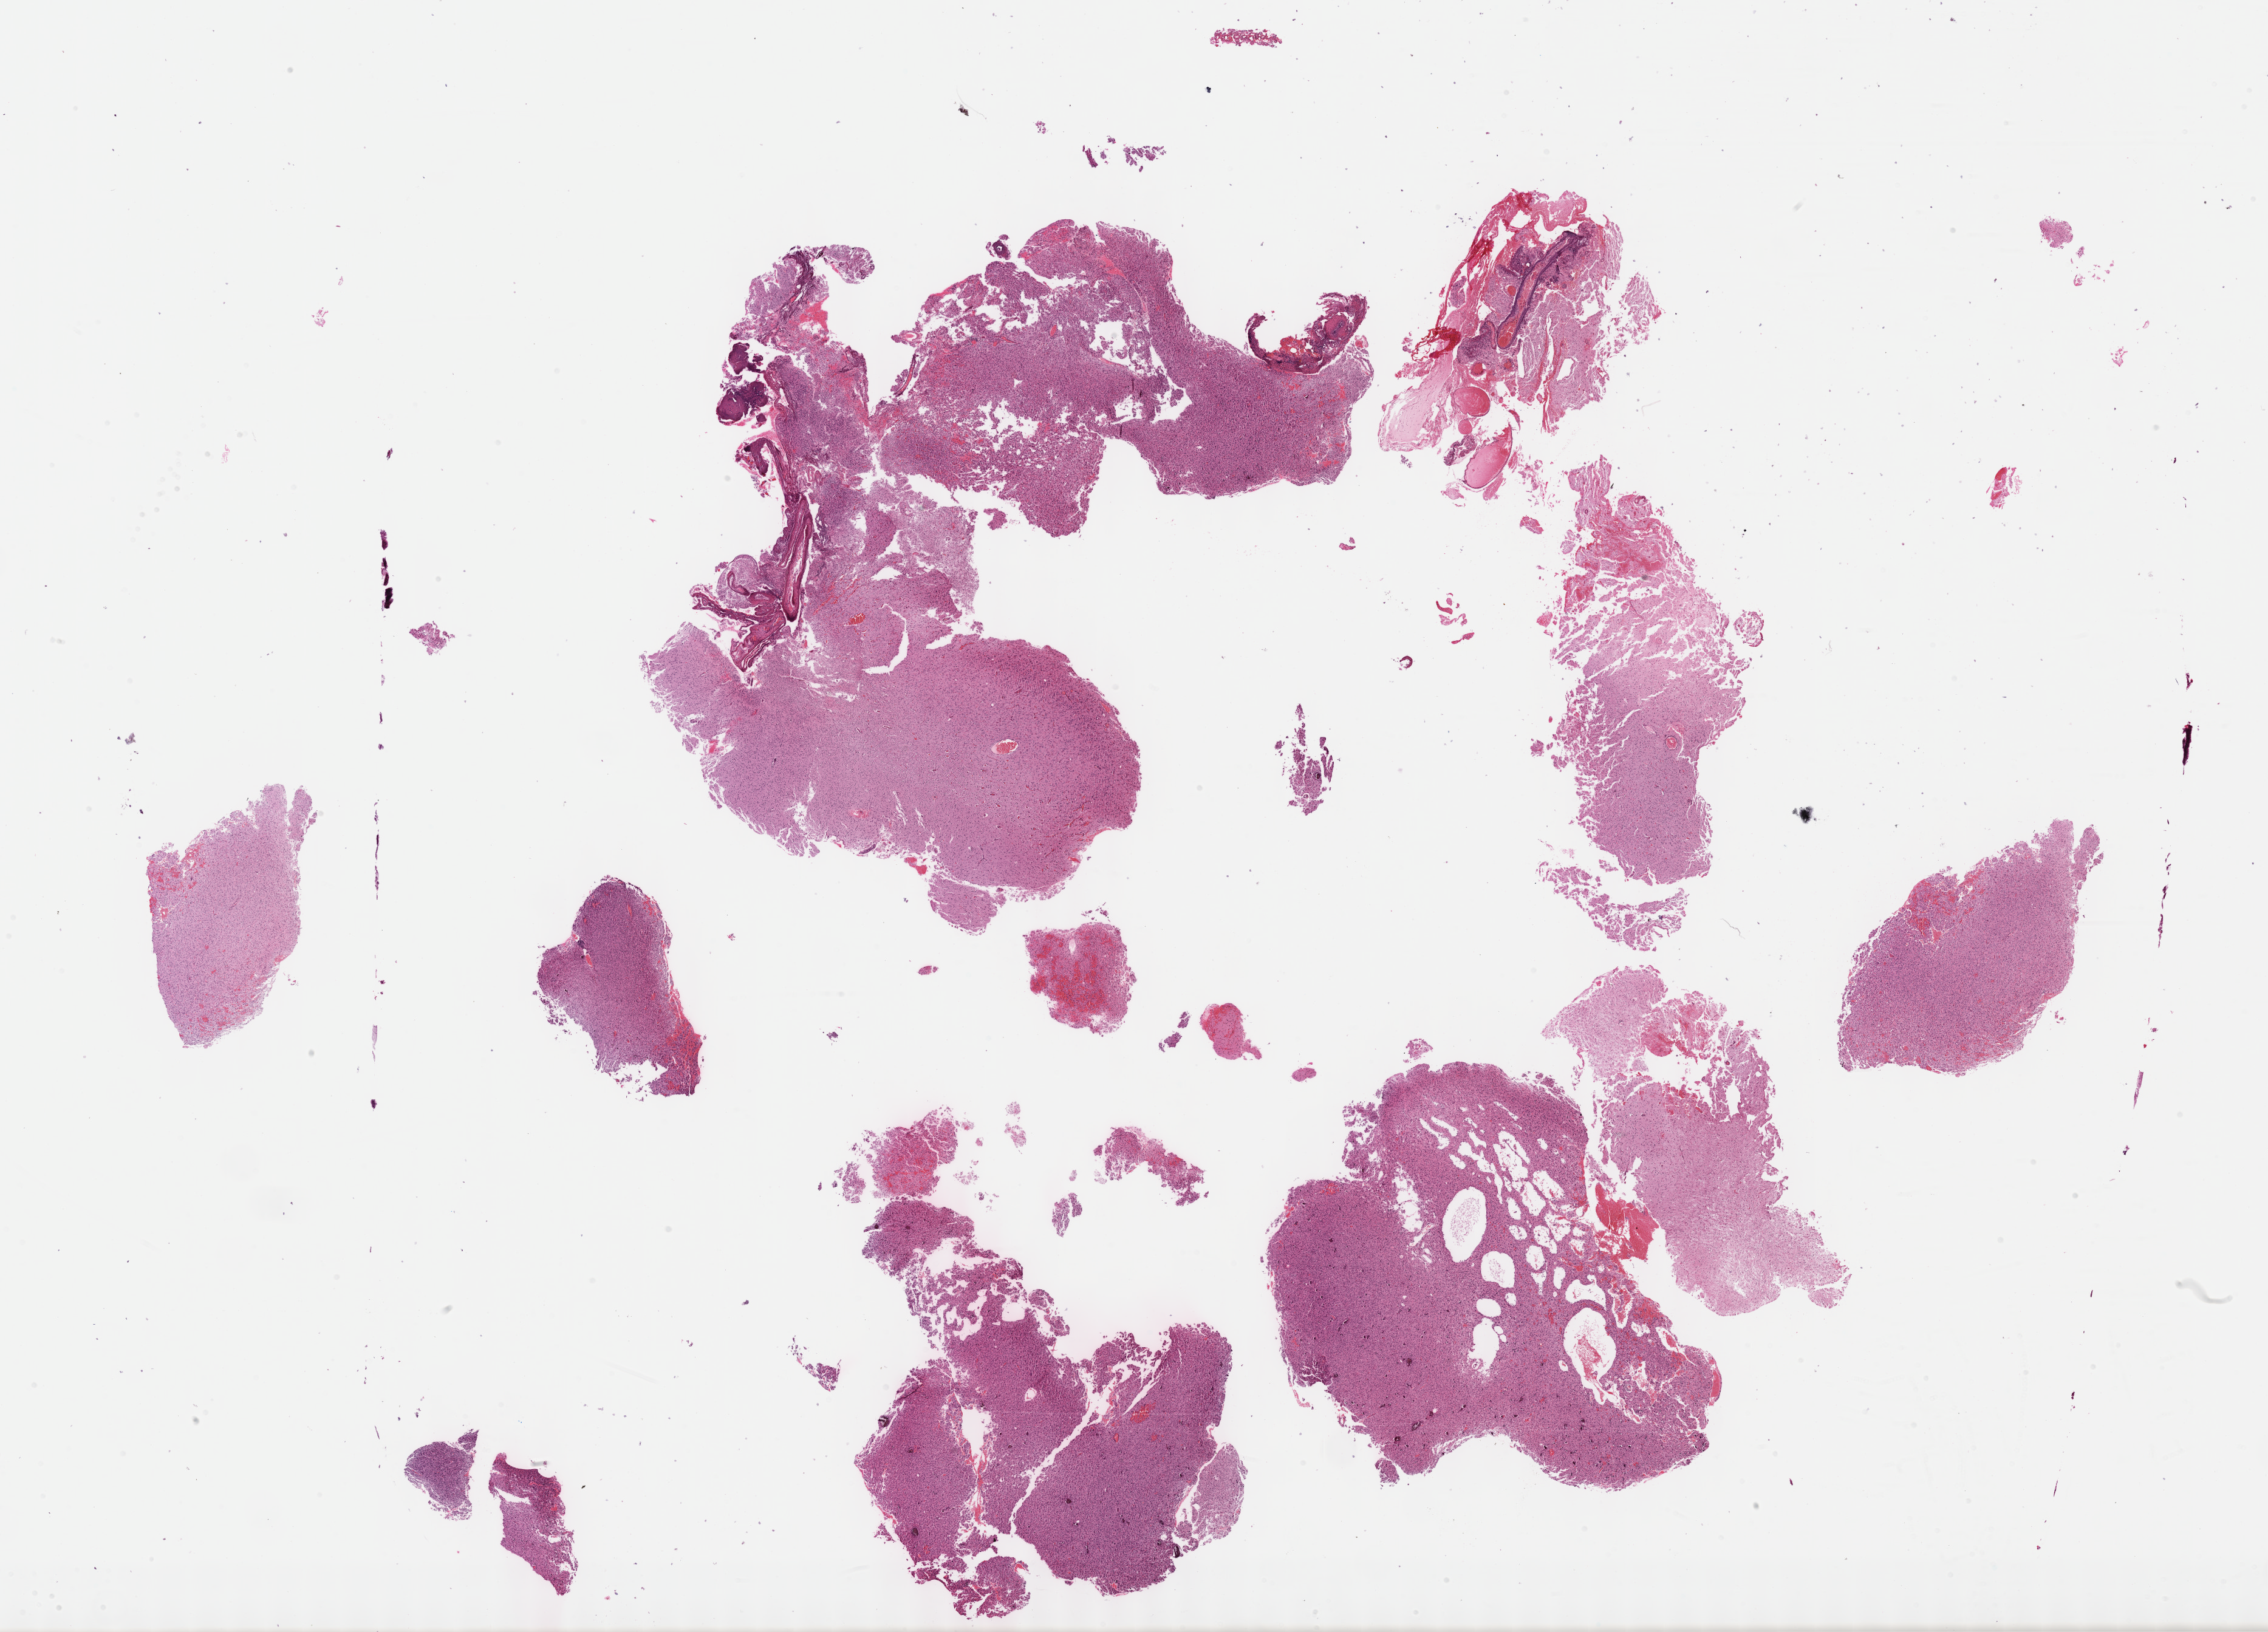
H&E whole-slide image — whole scanned area (about 30.2 x 21.7 mm) shown as a low-resolution overview; formalin-fixed paraffin-embedded (FFPE) diagnostic section; sample: primary tumour, brain. Male patient; age at initial diagnosis 40 years. Histologic grade: G3 (poorly differentiated).
Pathologic diagnosis: Astrocytoma, anaplastic (cerebrum). Laterality: left.